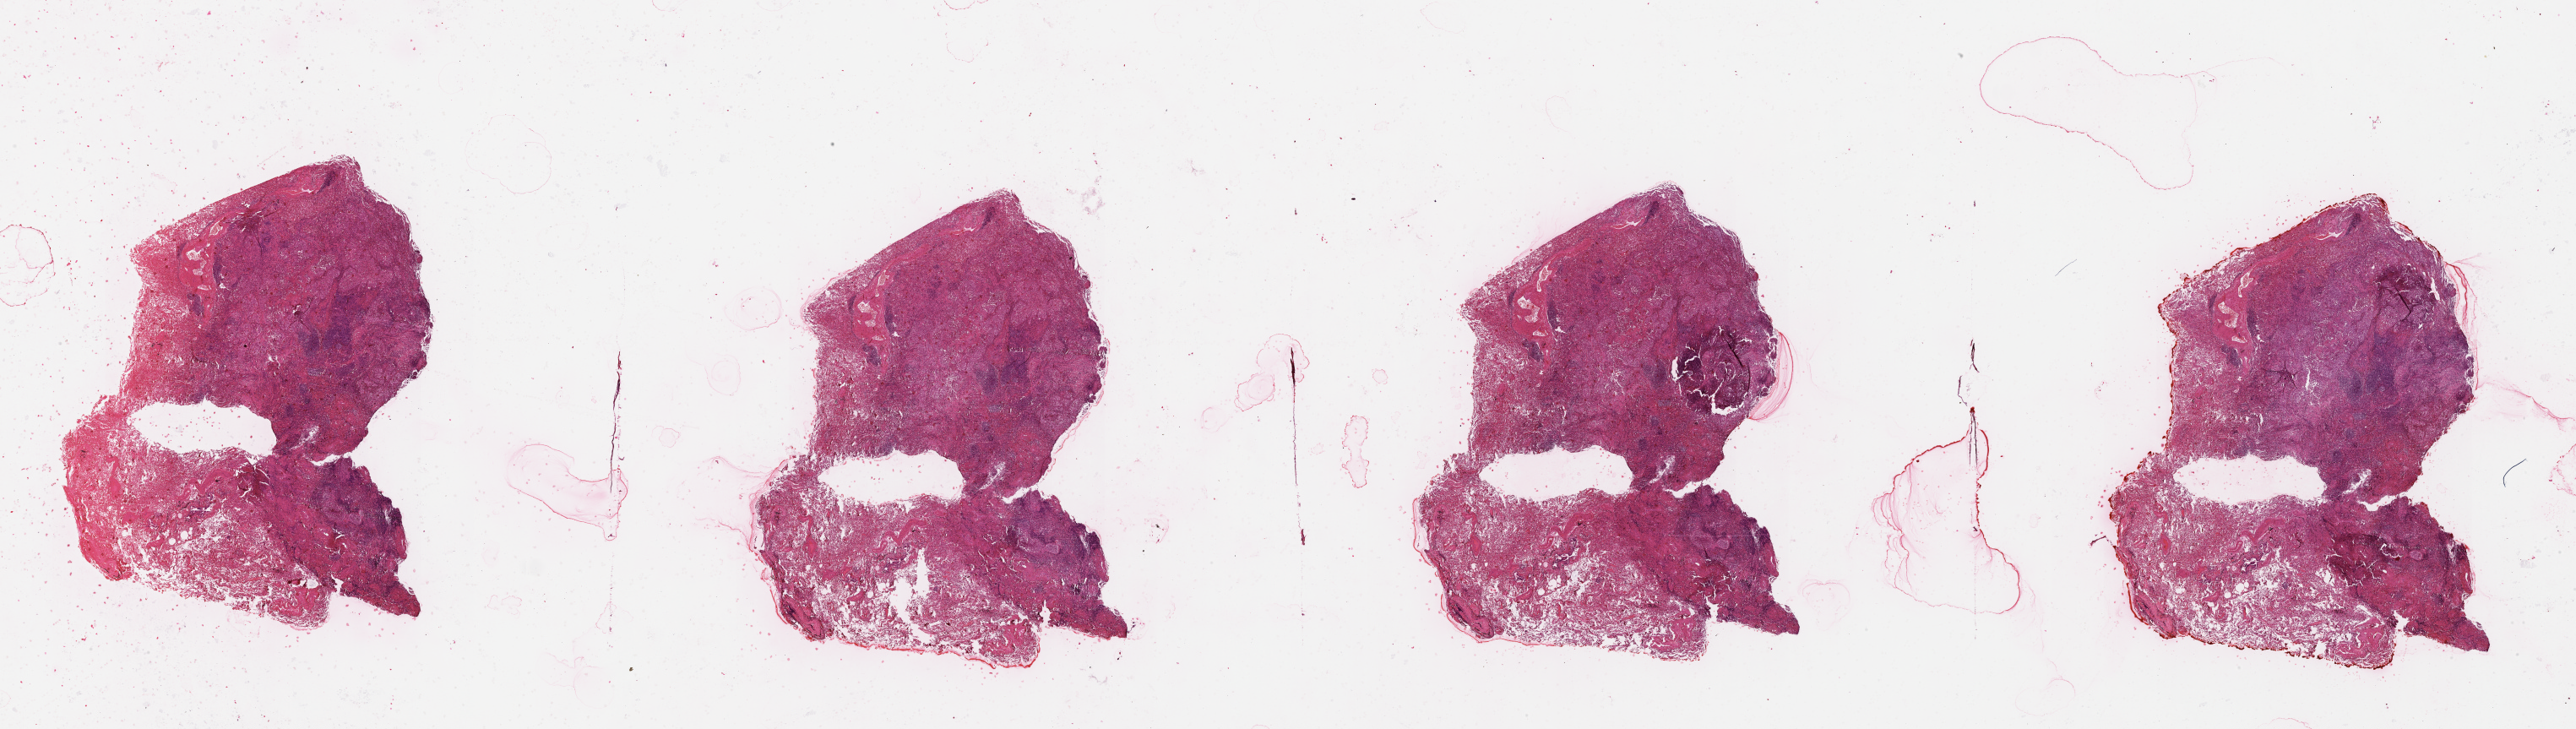
Digitized H&E-stained tissue section (whole slide) — a low-resolution overview of the entire scanned area, about 49.1 x 13.9 mm (from a 20x scan). Lung, tissue type not recorded.
Patient diagnosis (cohort enrolment): squamous cell carcinoma (lung).